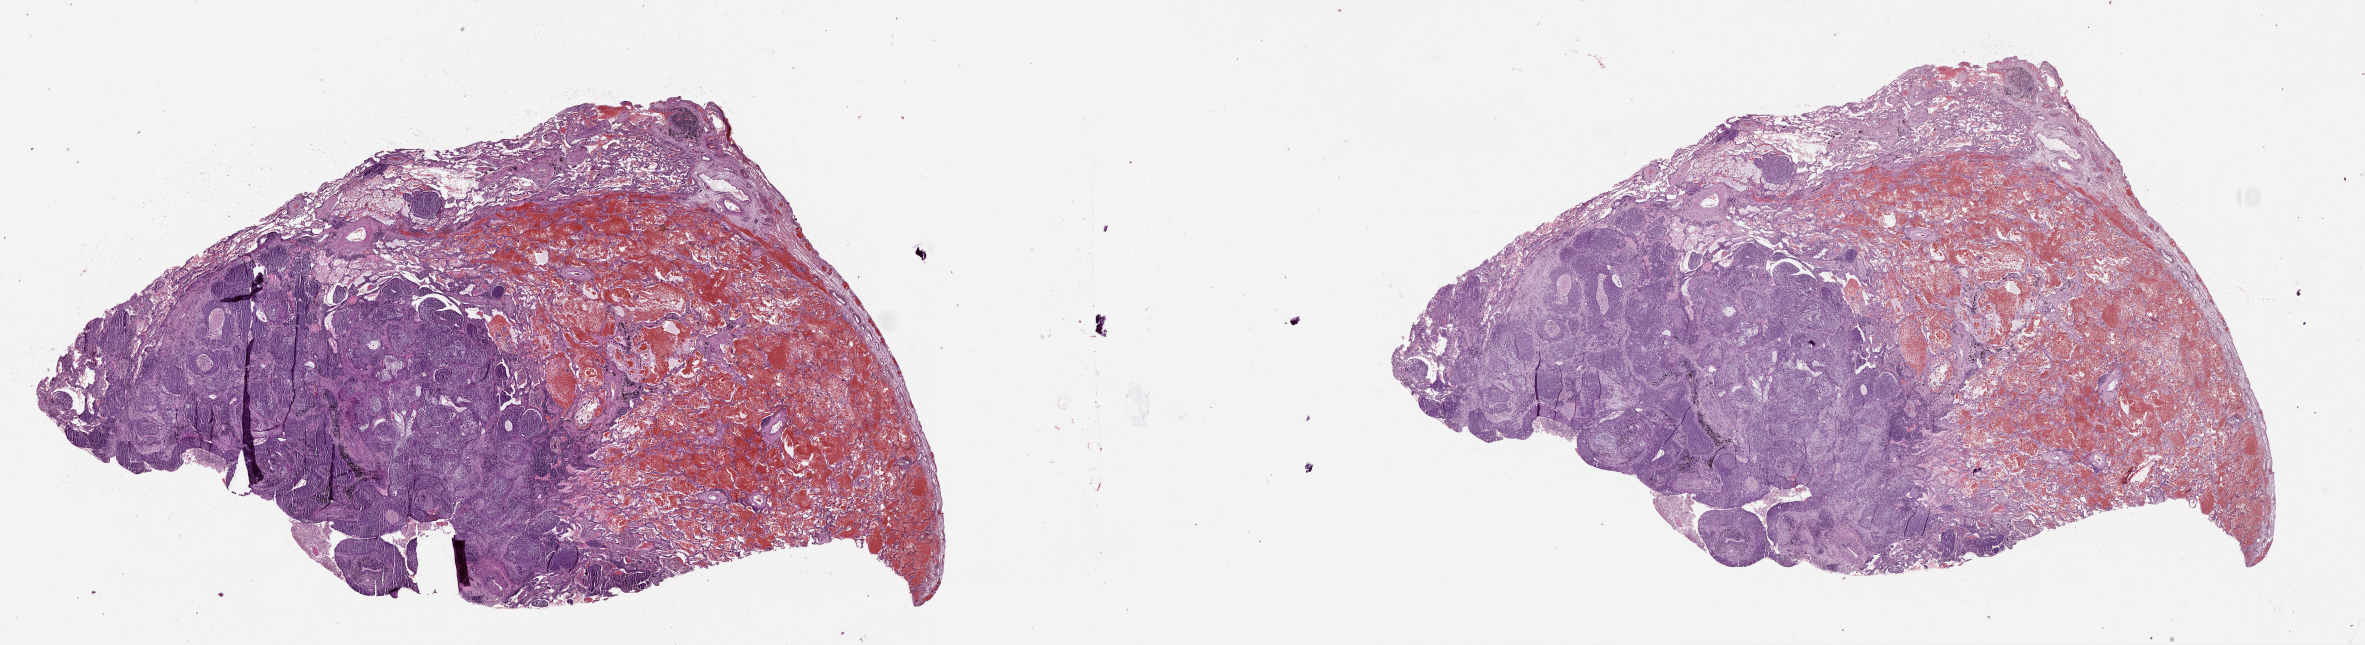
H&E-stained whole-slide image, low-resolution overview of the scanned area, about 38.1 x 10.4 mm. Tumour tissue sample, lung. Female, 63 y/o.
- patient diagnosis (cohort enrolment): squamous cell carcinoma (lung)